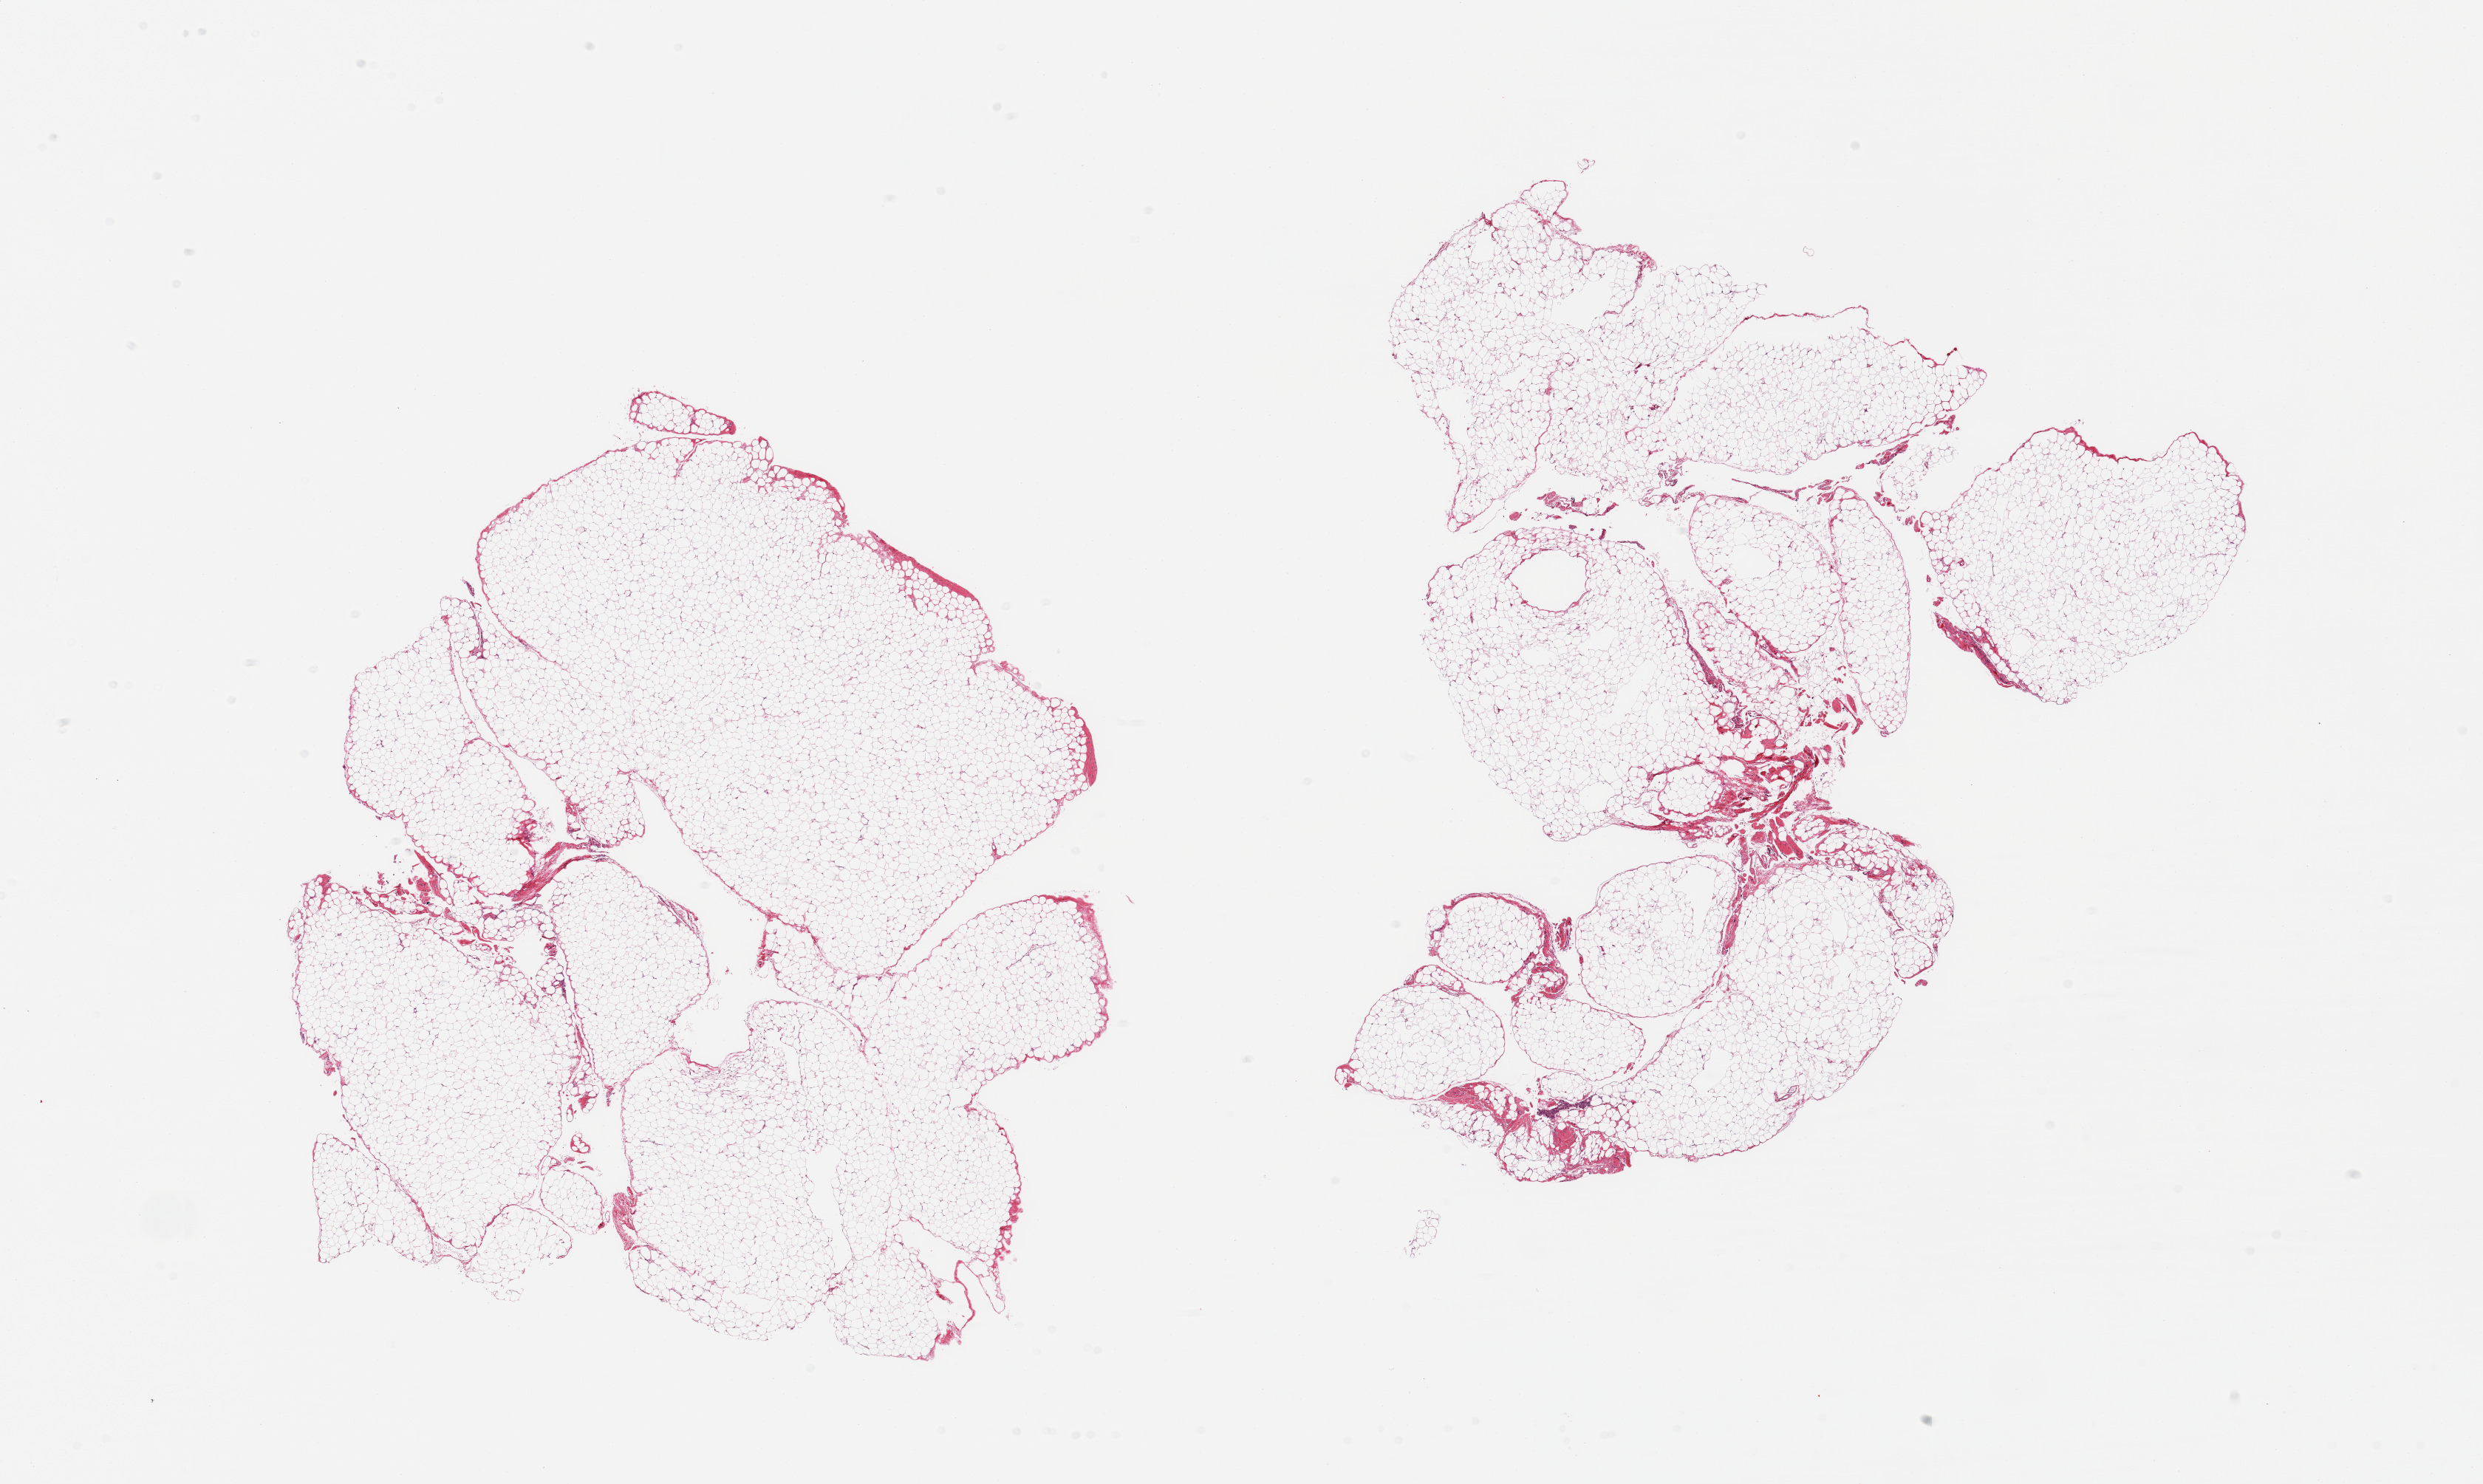
Whole-slide image, H&E stain, shown as a low-resolution overview of the whole scanned area (about 26.6 x 15.9 mm, from a 20x scan); PAXgene-fixed paraffin-embedded (PFPE) section; target tissue: omentum; donor tissue sample.
Reviewer comment on this tissue sample: 2 pieces; minimal fibrous content.